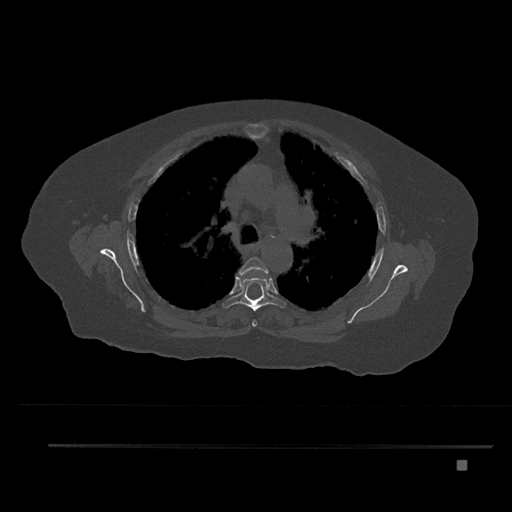
CT including the spine, one axial slice. Position 576 of 797 along the scan axis. Reconstruction kernel Br40s/3. 120 kVp. Bone window (W 1800 / L 400 HU). 0.5 mm slice thickness. 512 × 512 image matrix, field of view 437 × 437 mm. Patient: female, 76 years. Case-level facts recorded for this patient, not image findings: primary cancer: lung; vertebrae with lytic lesions (as recorded): T11, L3.
Structures marked on this image (semi-automatically segmented with operator editing):
- T4 vertebra: bounding box <238,257,268,327> (left, top, right, bottom; pixels)
- T5 vertebra: <222,277,286,311>